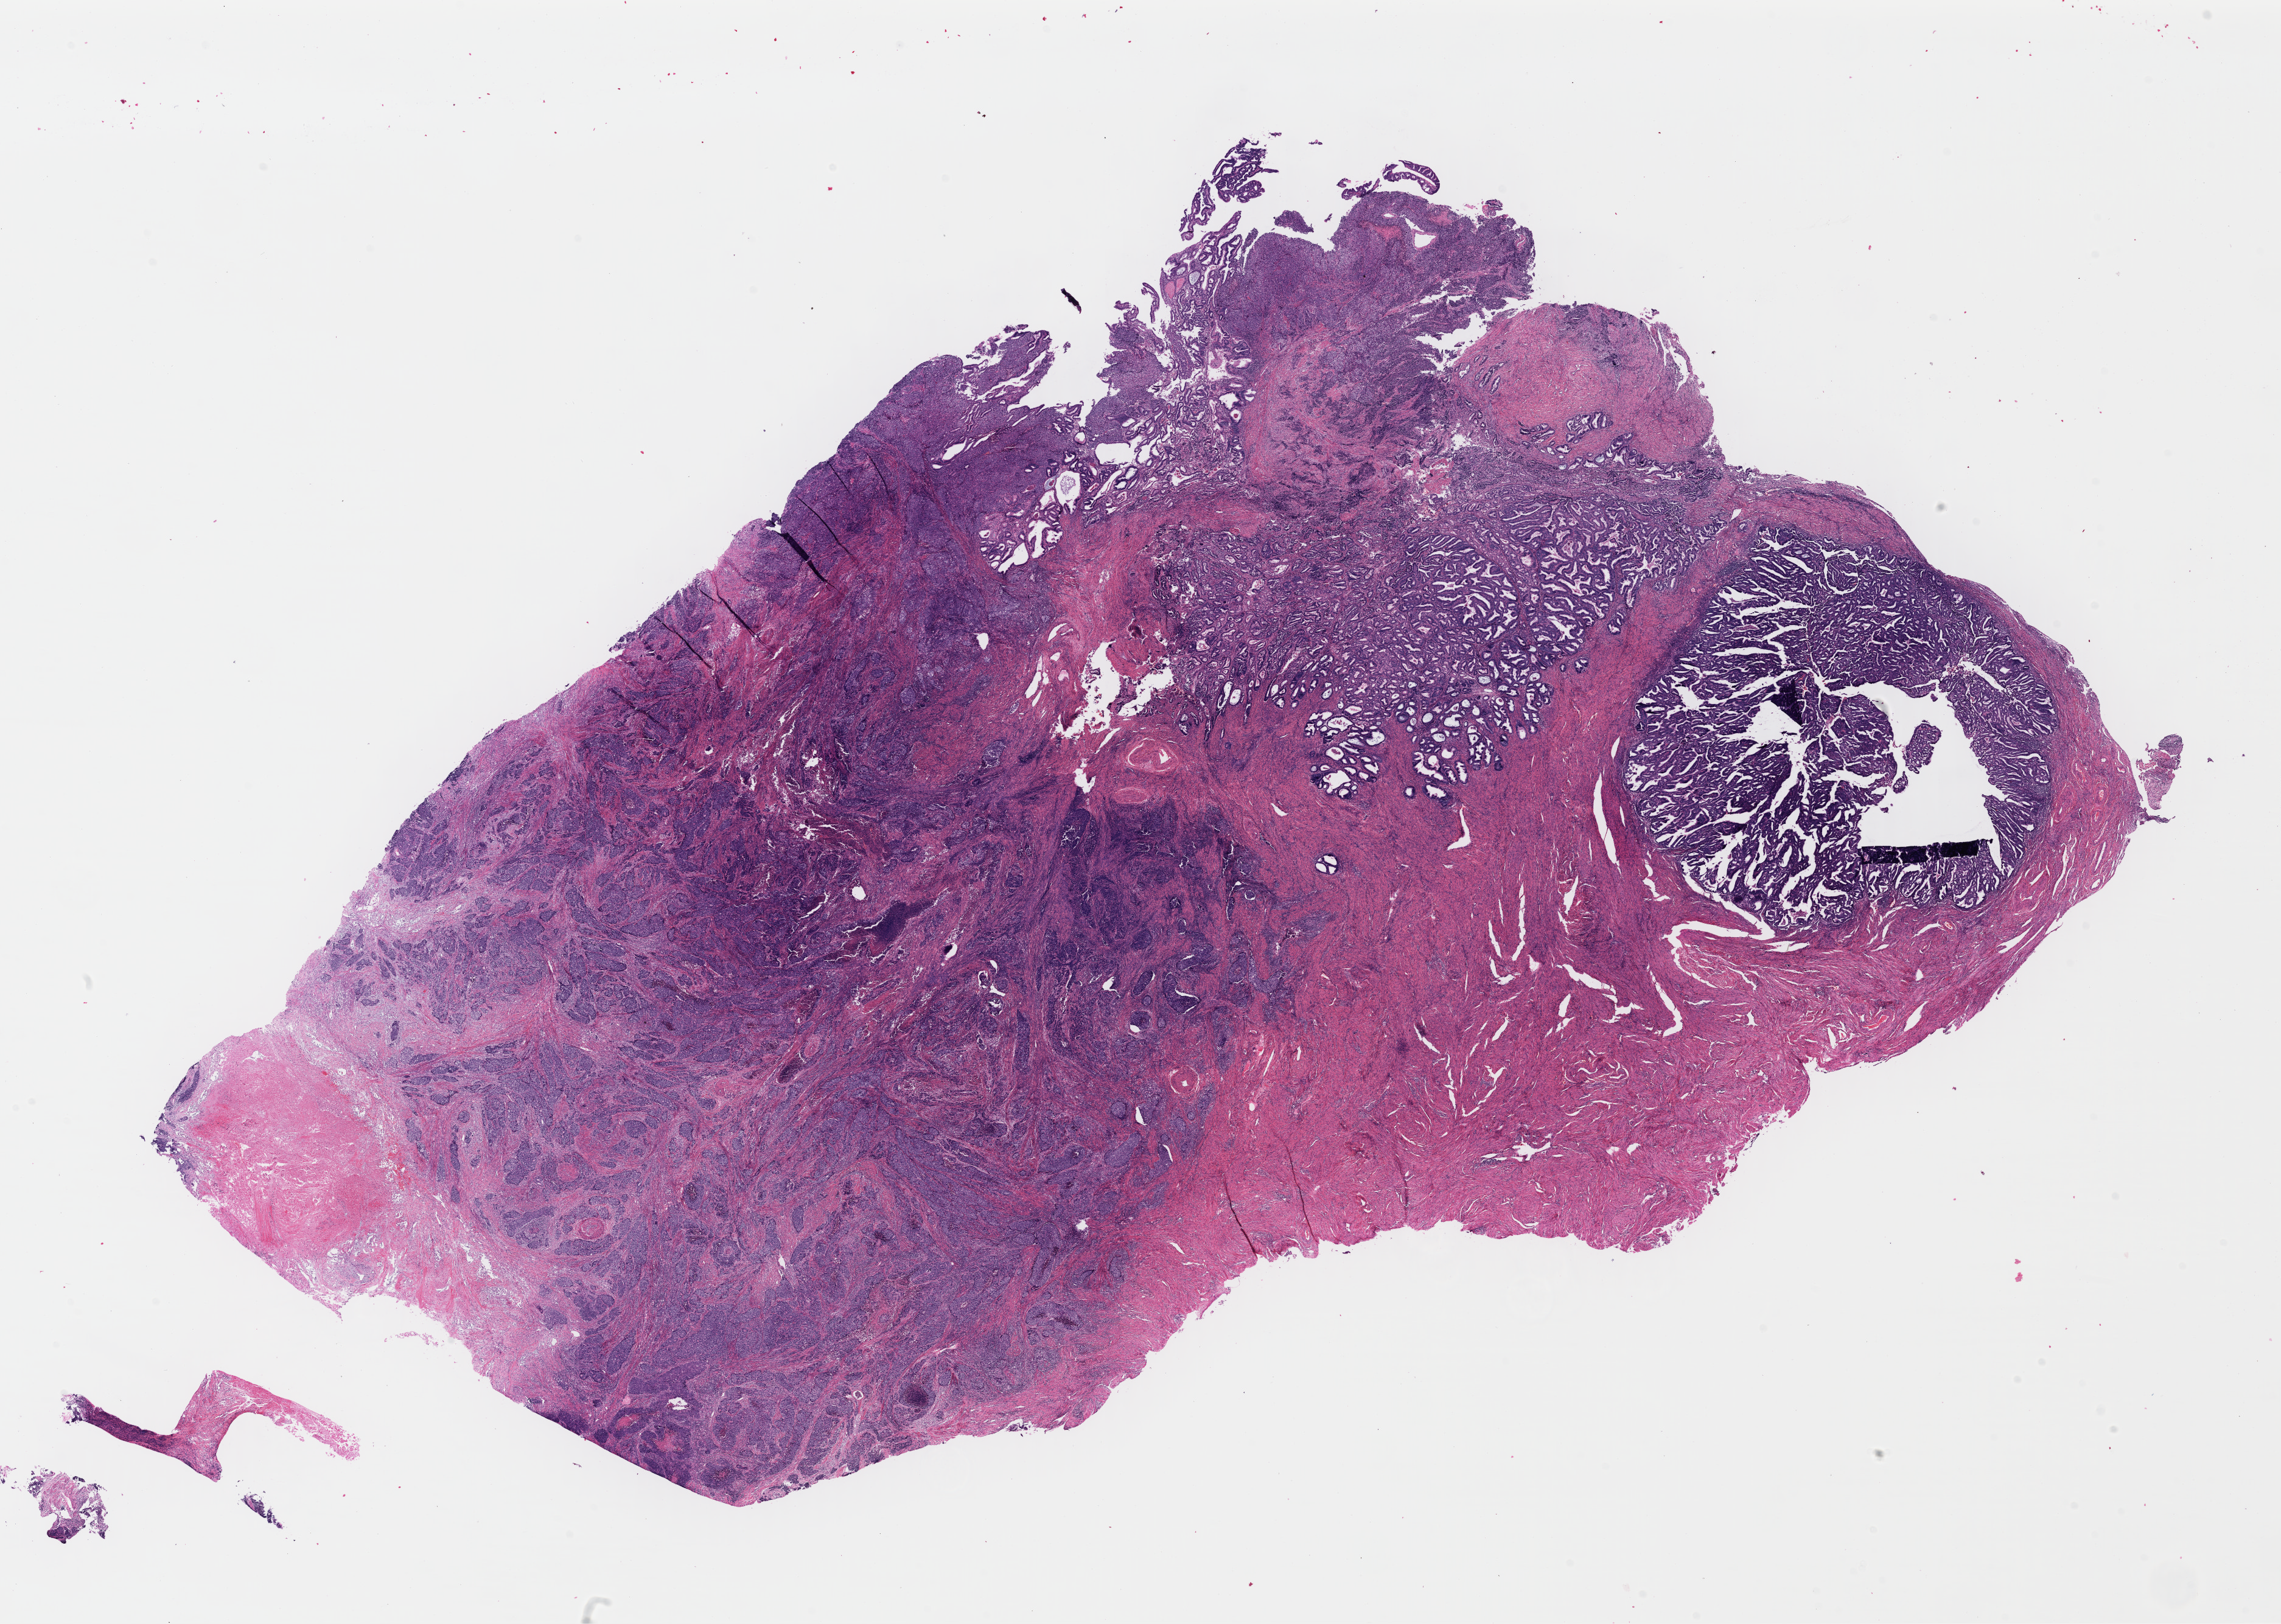
Digitized Hematoxylin and eosin (H&E) stained tissue section (whole slide), whole scanned area (about 29.5 x 21.0 mm, from a 40x scan) shown as a low-resolution overview; FFPE section; primary tumour sample from the uterus. Patient: female, age at initial diagnosis 47 years. Histologic grade: G3 (poorly differentiated).
FIGO stage: IB. Pathologic diagnosis: Endometrioid adenocarcinoma, NOS (endometrium).